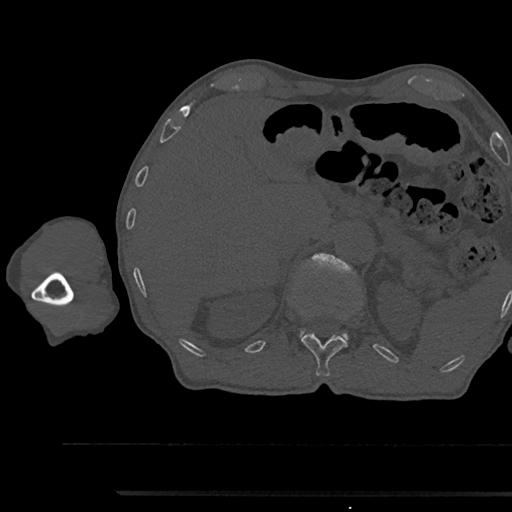
CT including the spine, one axial slice. Position 688 of 797 along the scan axis. 120 kVp. Bone window (W 1800 / L 400 HU). 0.5 mm slice thickness. 512 × 512 image matrix, field of view 367 × 367 mm. Patient: male, 79 years. From the clinical record (not read from this slice): primary cancer: prostate.
Outlined on this slice (semi-automatic segmentation, software-assisted and operator-edited):
- L1 vertebra: bounding box [x1, y1, x2, y2] px = [299, 254, 357, 341]
- T12 vertebra: [301, 333, 348, 377]